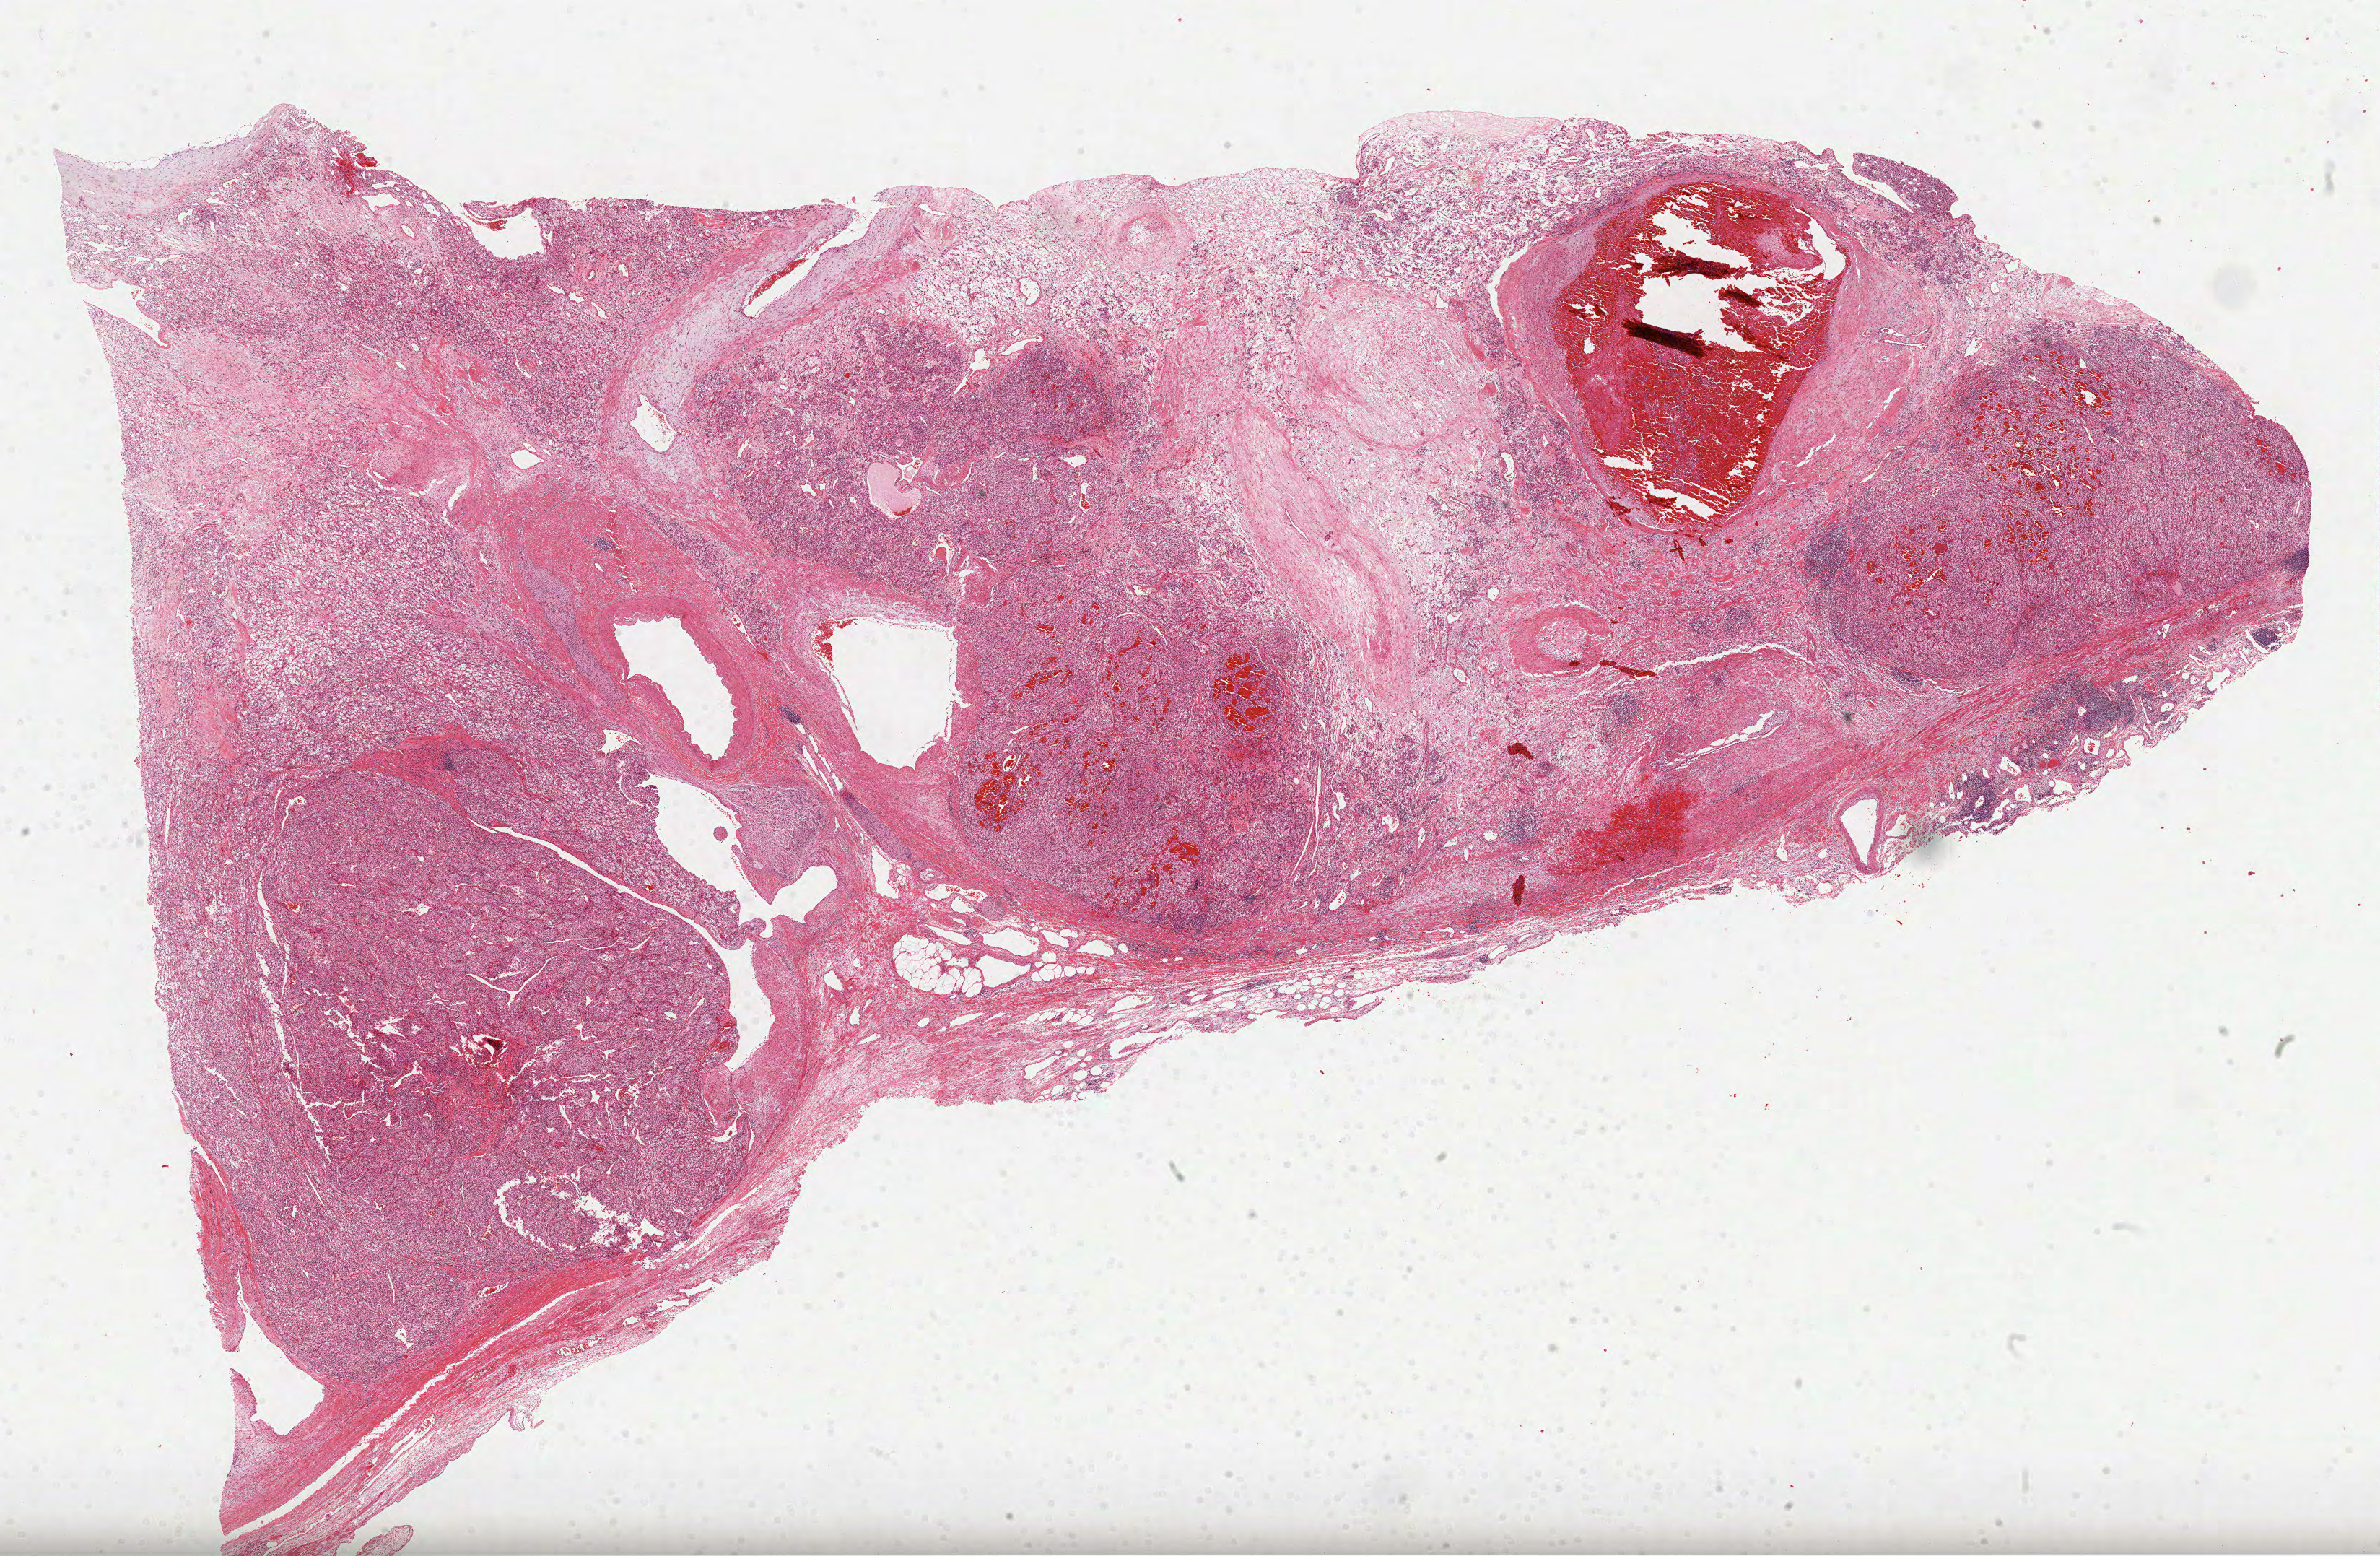
Hematoxylin and eosin (H&E) stained whole-slide image, shown as a low-resolution overview of the whole scanned area (about 26.6 x 17.4 mm); formalin-fixed paraffin-embedded (FFPE) diagnostic section; primary tumour sample from the kidney. Female, age 75 years at initial diagnosis.
Diagnosis: Clear cell adenocarcinoma, NOS.